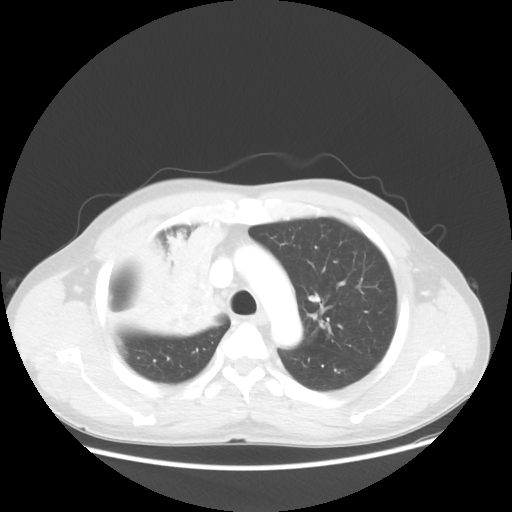
Chest CT, one axial slice; position 40 of 56 along the scan axis; reconstruction kernel STANDARD; lung window (W 1500 / L -600 HU); 512 × 512 image matrix, field of view 398 × 398 mm. Patient: male, 60 years. Case-level facts recorded for this patient, not image findings: clinical TNM (as recorded): T2a N1 M0.
Outlined on this slice (rectangle marked by the reading radiologist):
- lung tumour (recorded histology: squamous cell carcinoma): bounding box (x1, y1, x2, y2) in pixels: (121, 227, 235, 345)